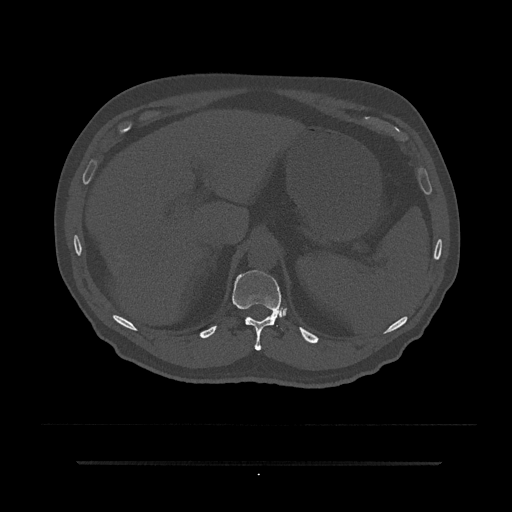
CT including the spine, one axial slice; slice 262 of 797 in the series (ordered by position); reconstruction kernel Br40s/3; 120 kVp; bone window (W 1800 / L 400 HU); 0.5 mm slice thickness; 512 × 512 image matrix, field of view 464 × 464 mm. Male patient, age 59 years. Case-level facts recorded for this patient, not image findings: primary cancer: bile ducts; vertebrae with lytic lesions (as recorded): T10.
Structures marked on this image (semi-automatically segmented with operator editing):
- T11 vertebra: bounding box (x1, y1, x2, y2) in pixels: (232, 270, 285, 351)